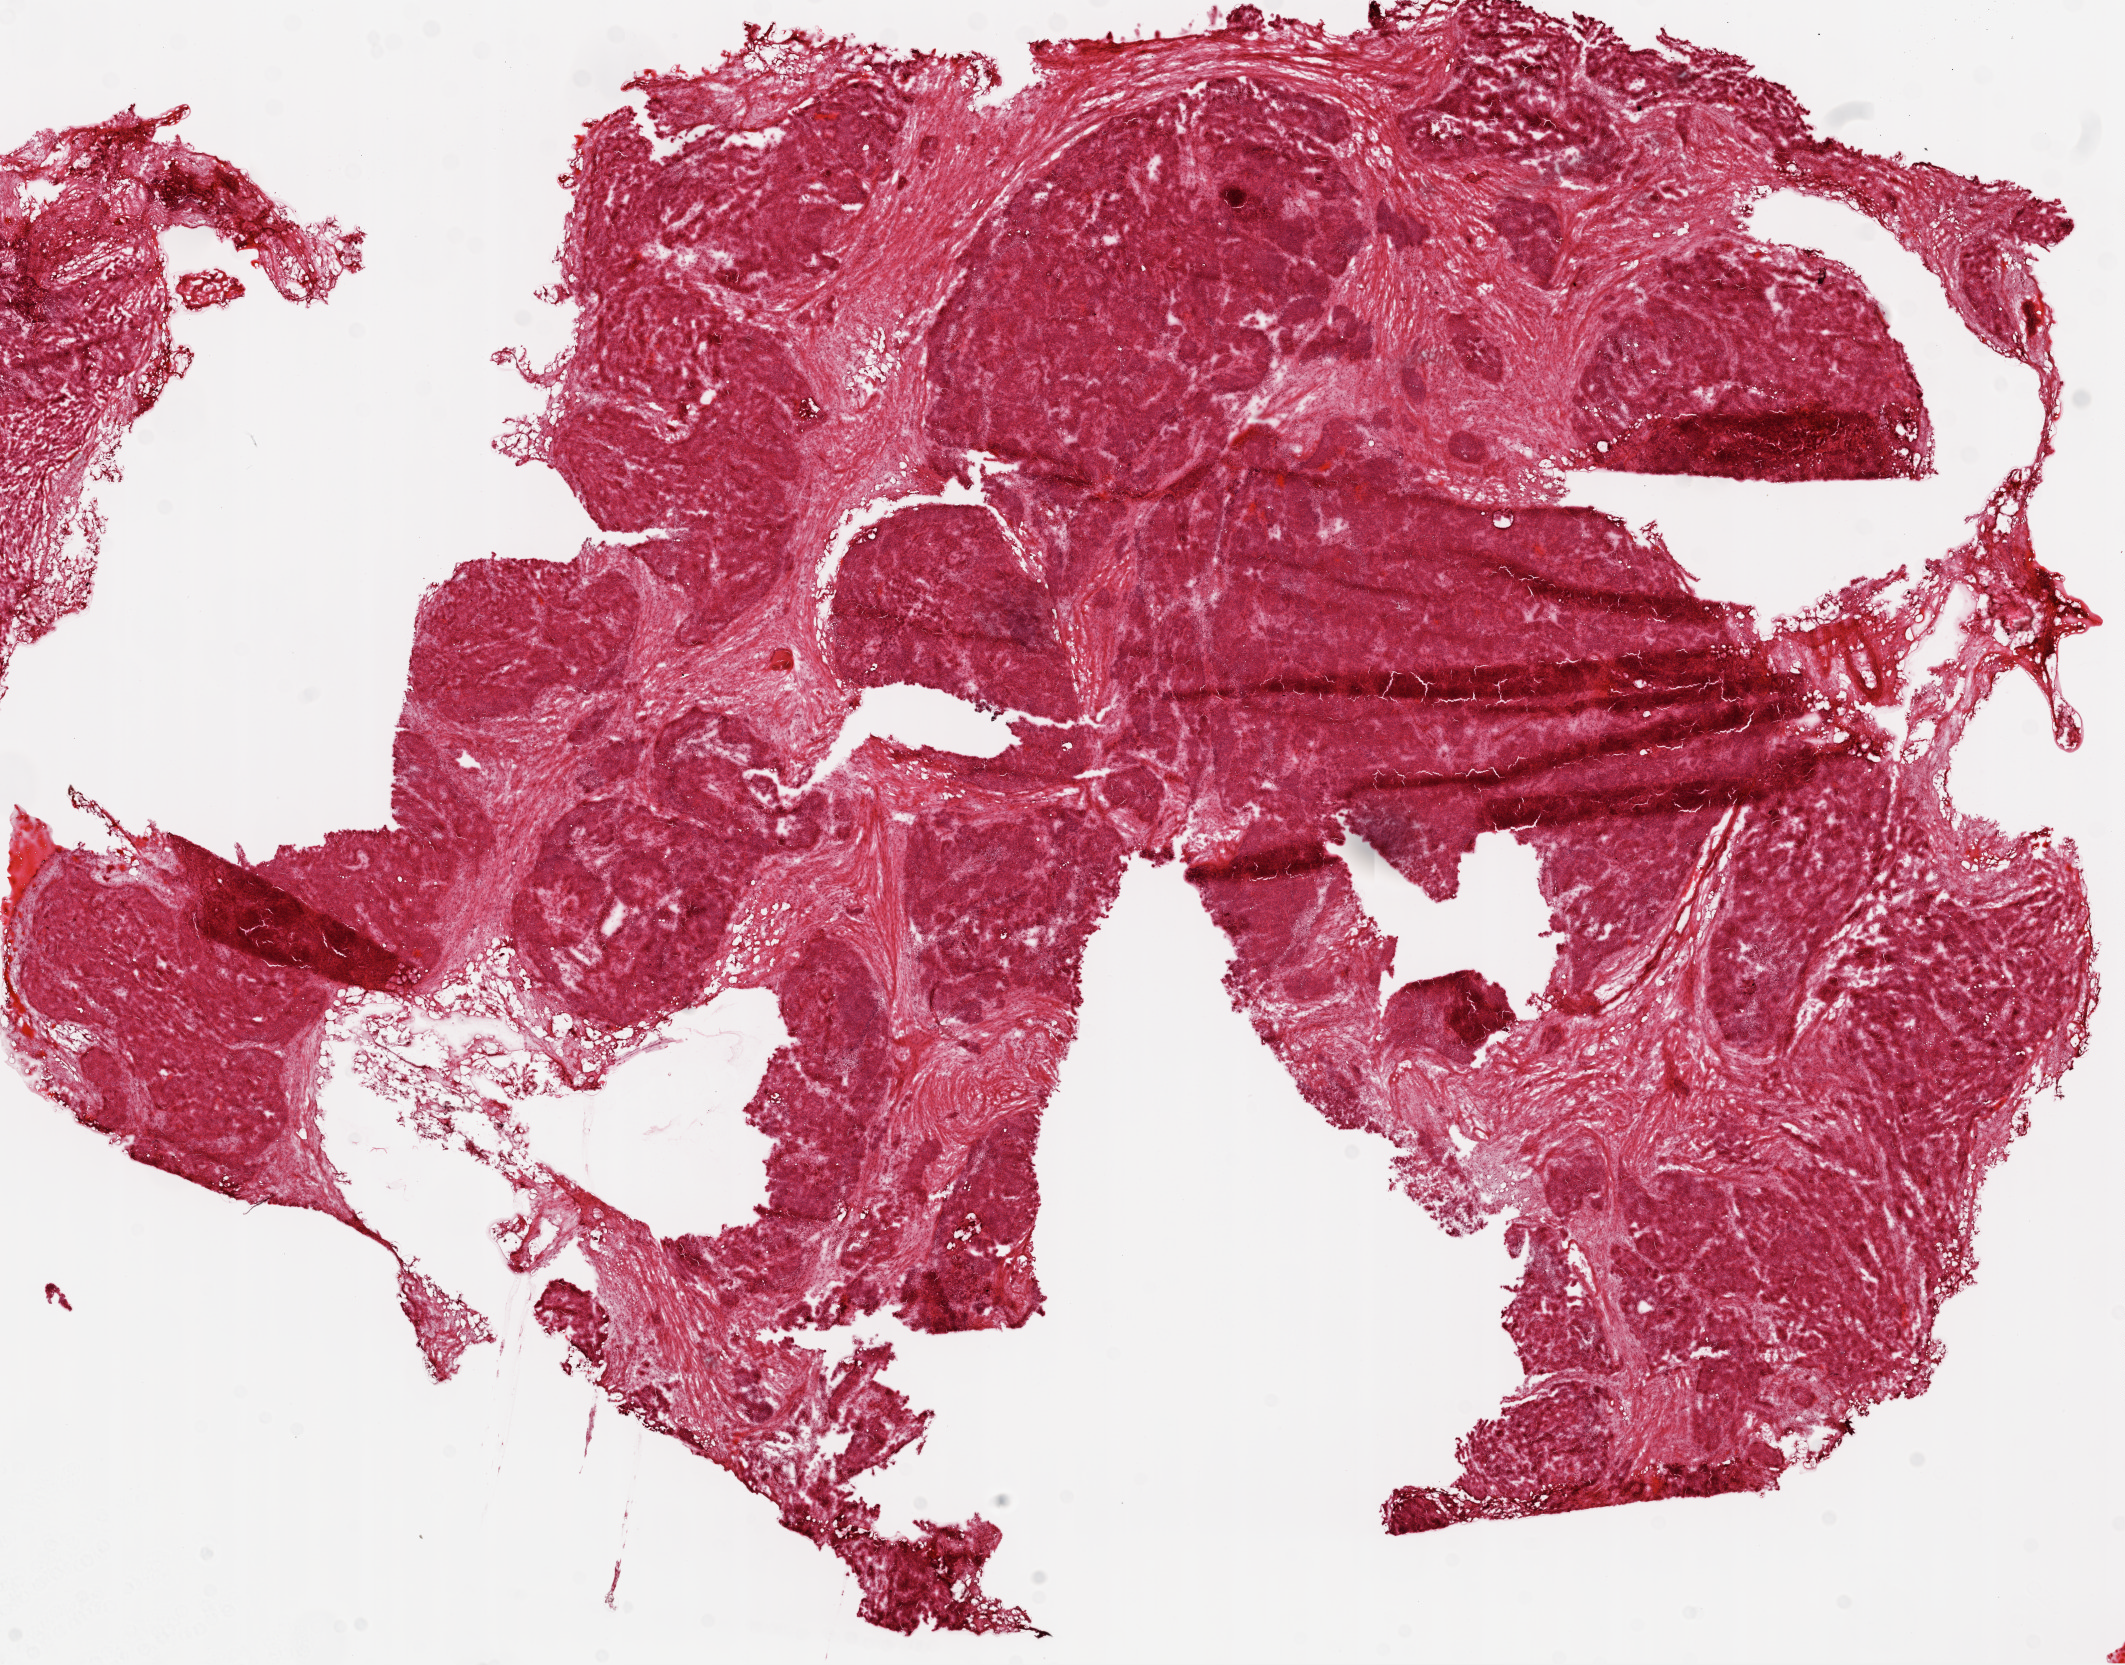
H&E whole-slide image — a low-resolution overview of the entire scanned area, about 17.1 x 13.4 mm (slide scanned at 20x); frozen section from the top of the tissue portion; ovary, primary tumour sample. Female, age 70 years at initial diagnosis. Histologic grade: G3 (poorly differentiated). Composition of this section per pathologist review: tumour cells 75%, tumour nuclei 75%, normal cells 0%, stromal cells 24%, necrosis 1%.
Pathologic diagnosis: Serous cystadenocarcinoma, NOS. FIGO stage: IIIC. Laterality: bilateral.